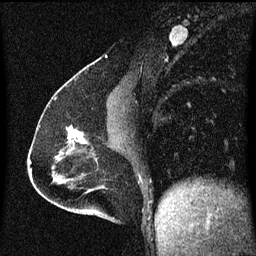
Breast MRI (dynamic contrast-enhanced), one sagittal slice; slice 26 of 60 in the series (ordered by position); dynamic contrast-enhanced series, image 2 of 3 at this slice position (ordered by acquisition); 1.5 T; TE 4.2 ms, TR 8 ms; 256 × 256 image matrix, field of view 200 × 200 mm. Patient: female, 51 years.
Annotated regions visible in this slice (semi-automatic segmentation, software-assisted and operator-edited):
- analysis volume of interest (the breast-tissue region the enhancement analysis was run in; not a lesion): box from (x=64, y=126) to (x=93, y=149) px
- tumour enhancement mask (voxels above the 70 % enhancement threshold inside the analysis volume of interest): (x=66, y=126)–(x=83, y=143)